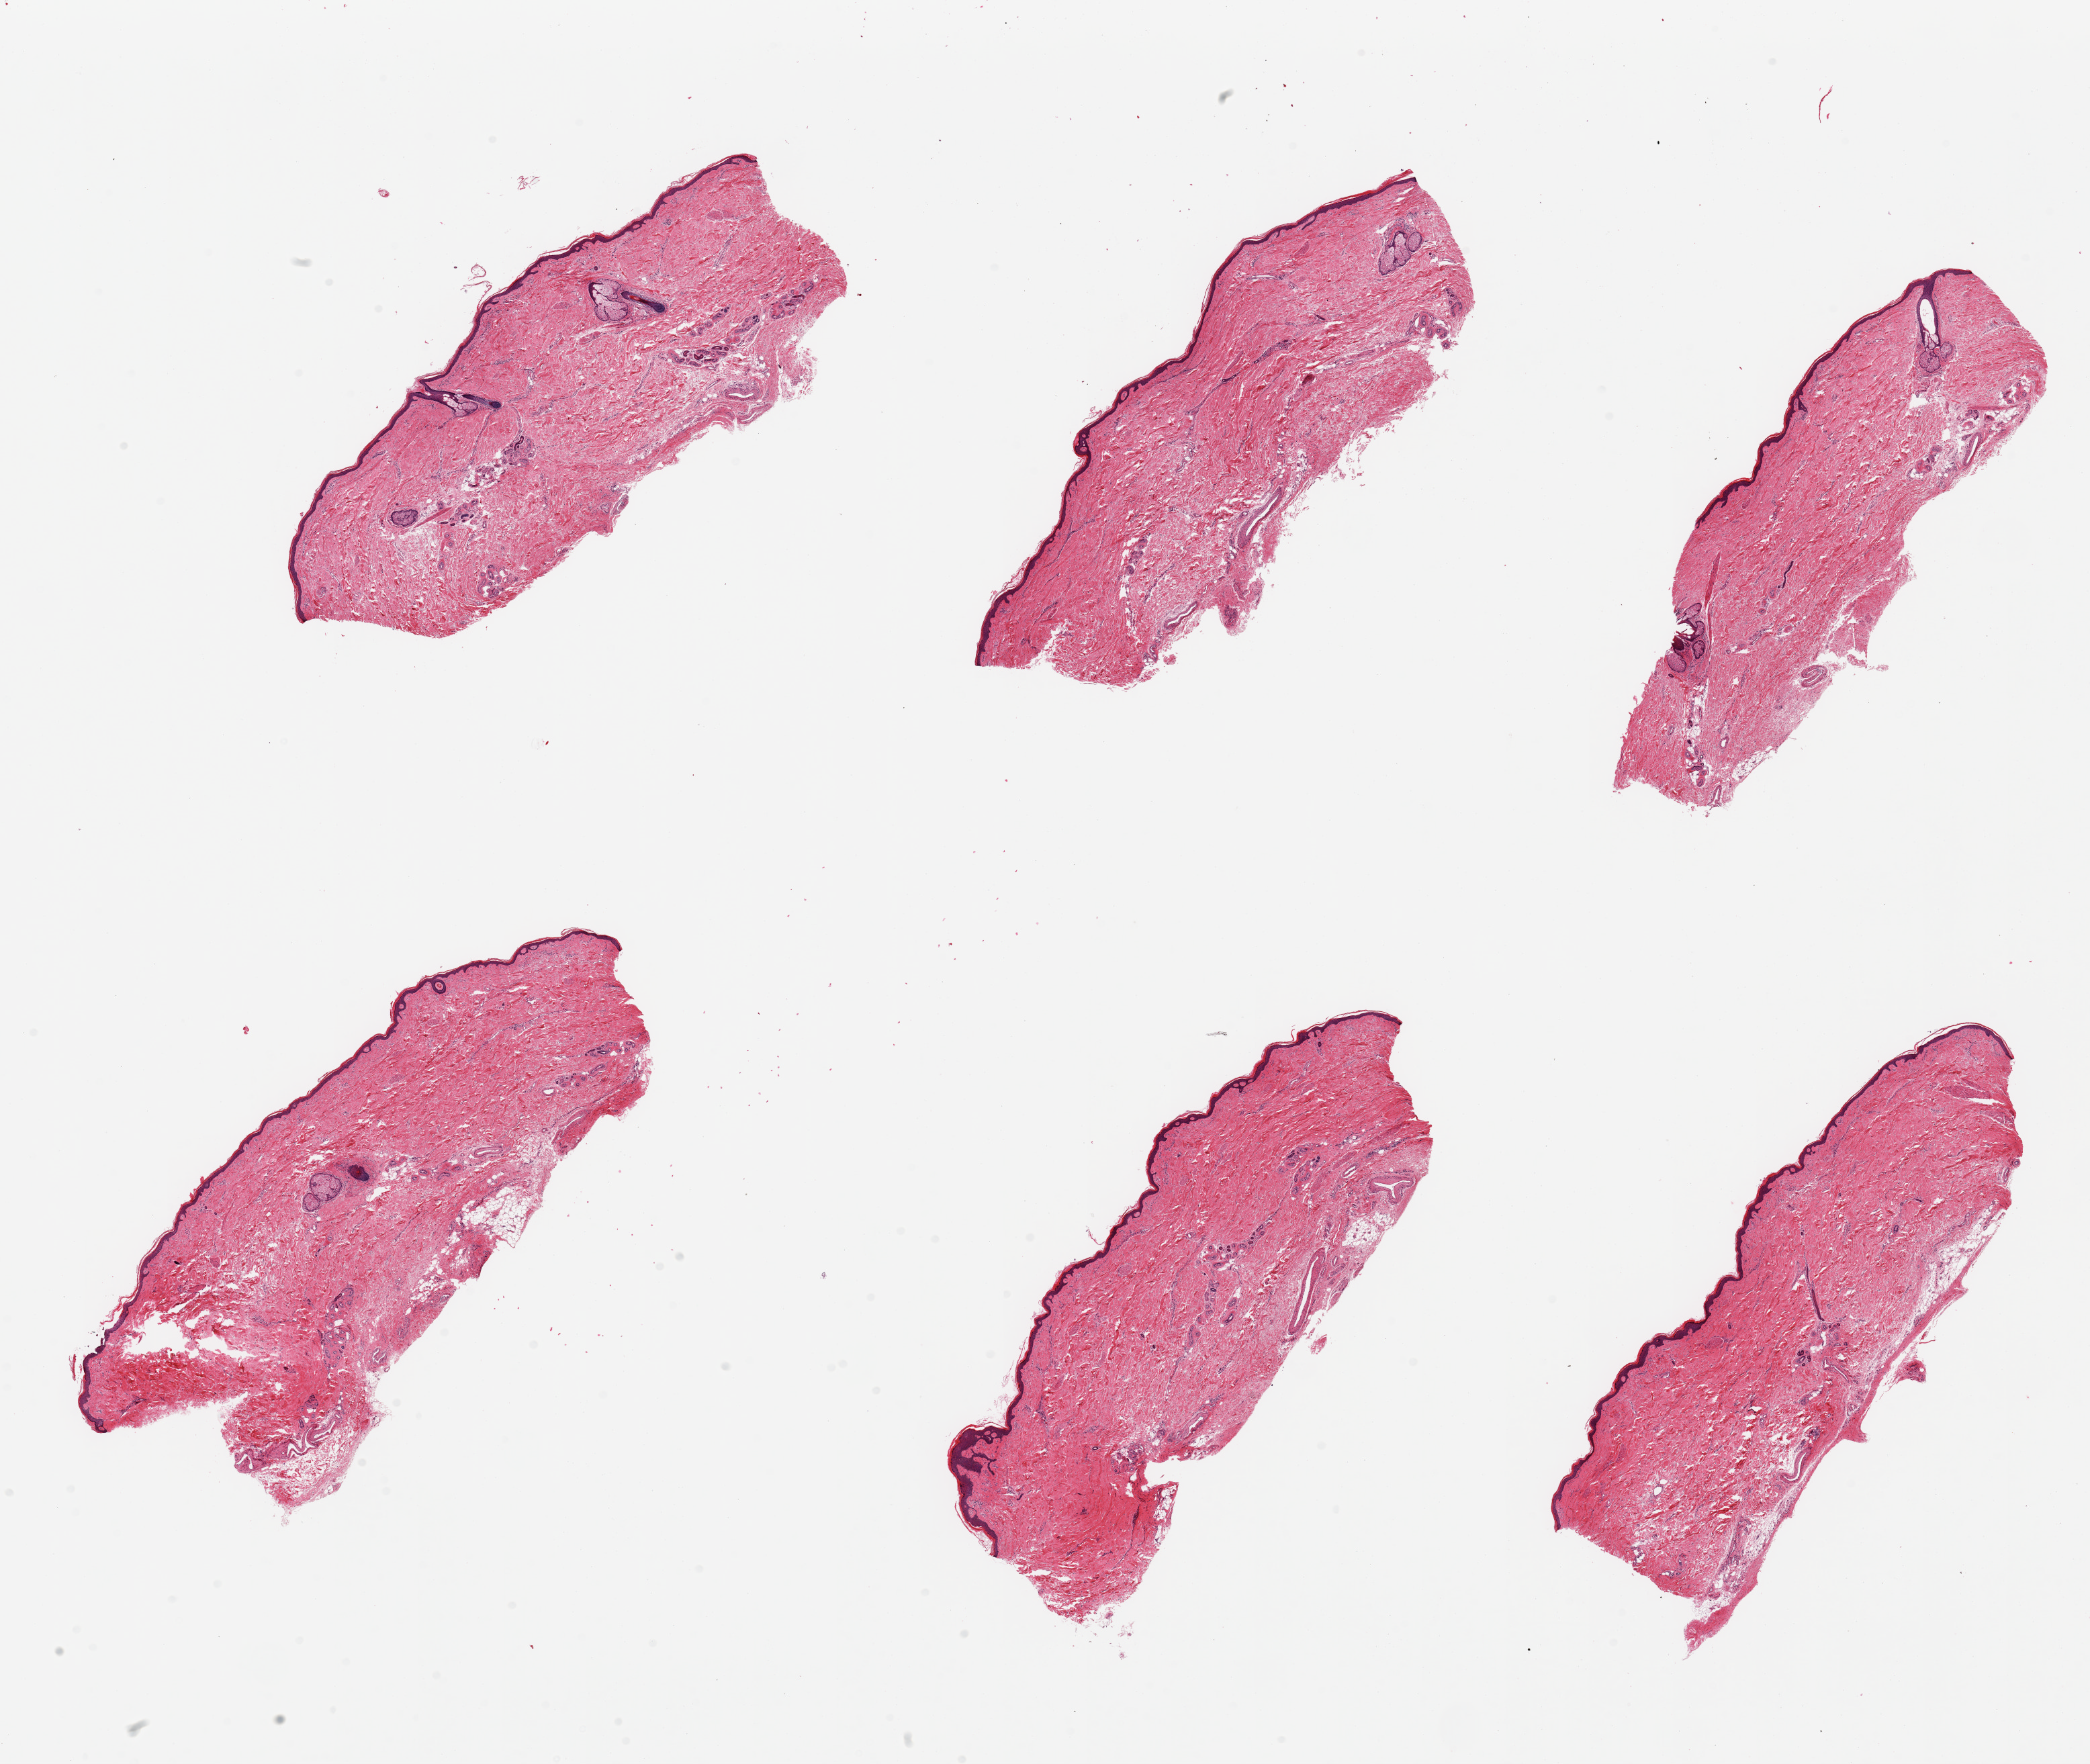
H&E whole-slide image, whole scanned area (about 24.6 x 20.8 mm, acquisition: 20x scan) shown as a low-resolution overview, PAXgene-fixed paraffin-embedded (PFPE) section, target tissue: skin of lower leg, tissue donor sample.
Reviewer comment on this tissue sample: 6 pieces, minimal dermal fat; squamous epithelium is ~60-70 microns.